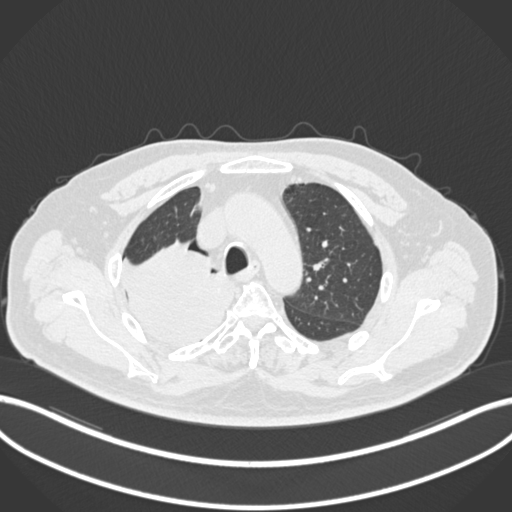
Chest CT, one axial slice; 120 kVp; lung window (W 1500 / L -600 HU); 1 mm slice thickness; 512 × 512 image matrix. Patient: male, 68 years. Case-level facts recorded for this patient, not image findings: clinical TNM (as recorded): T2a N0 M0.
Annotated regions visible in this slice (bounding box drawn by a radiologist):
- lung tumour (recorded histology: adenocarcinoma): box from (x=114, y=242) to (x=231, y=351) px